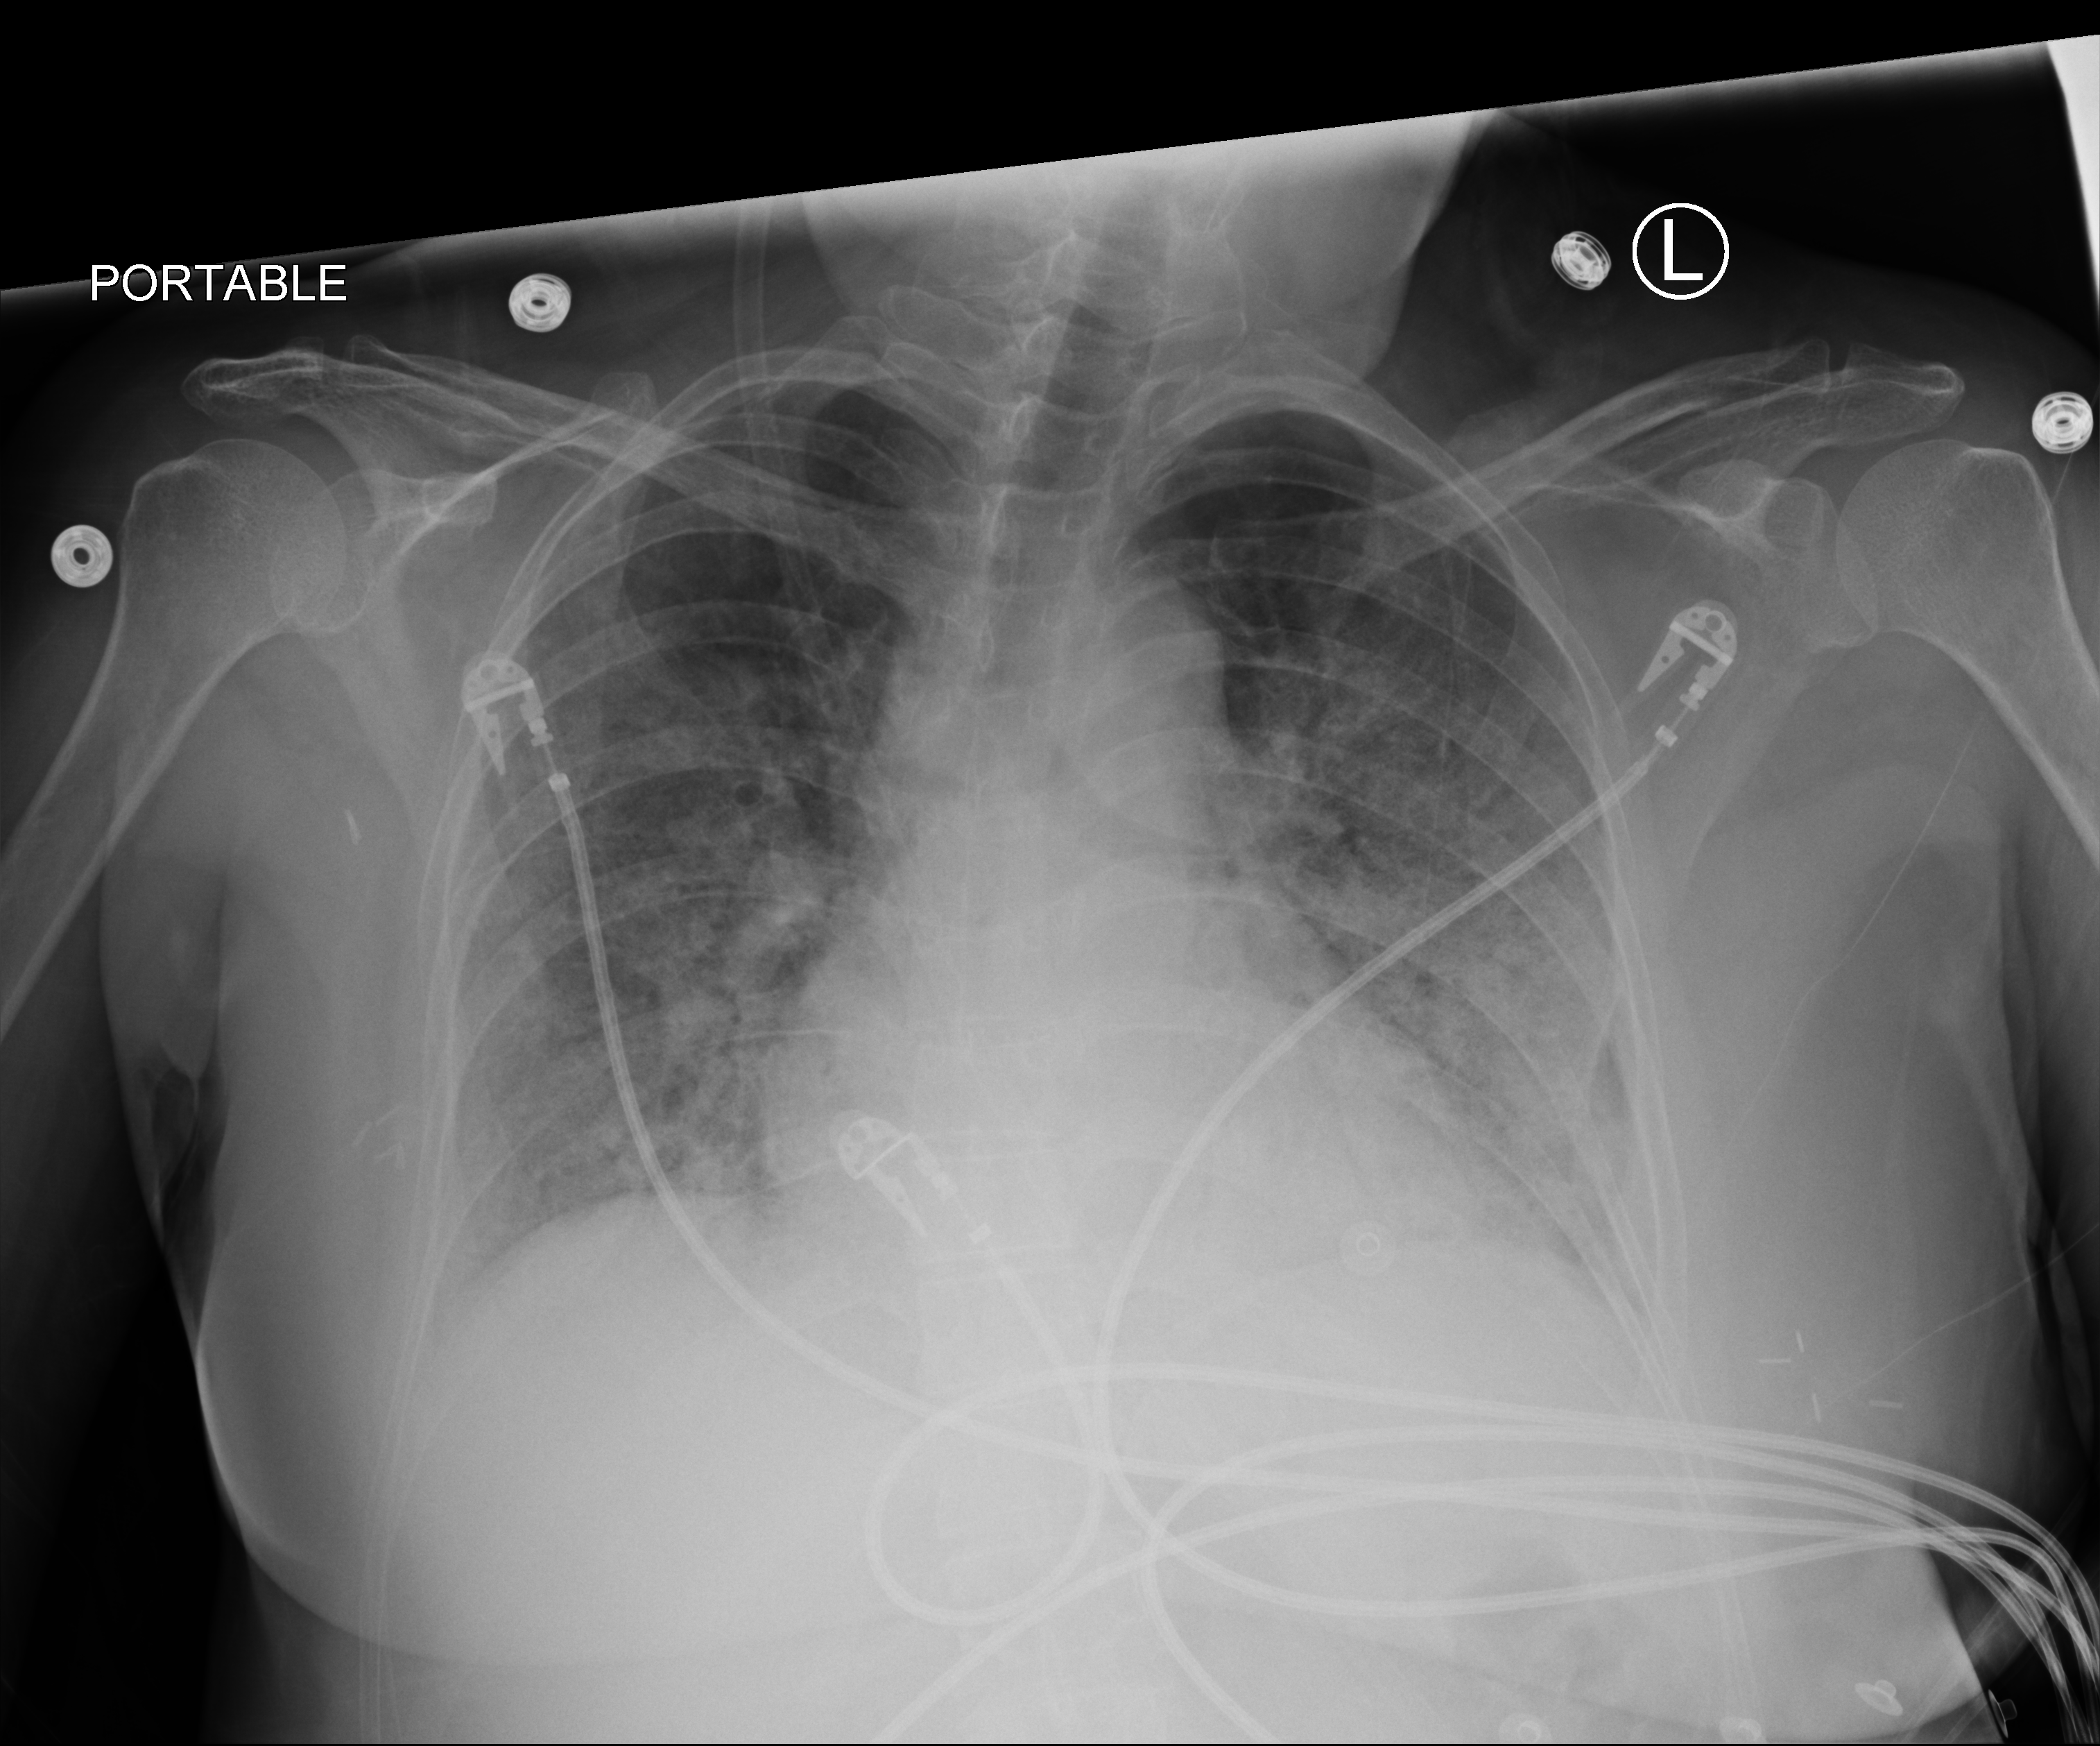
Chest X-ray (portable); anteroposterior (AP) projection. Patient hospitalised with COVID-19; female, aged 18–59 years.
Hospital-stay facts (about this admission, not read from this image; timing relative to this image not recorded):
- mechanically ventilated during this hospital stay: yes
- length of hospital stay: 21 days